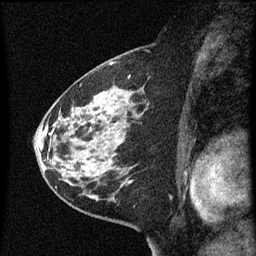
Breast MRI (dynamic contrast-enhanced), one sagittal slice. Position 33 of 60 along the scan axis. Dynamic contrast-enhanced series, image 2 of 3 at this slice position (ordered by acquisition). 1.5 T. TE 4.2 ms, TR 8 ms. 2 mm slice thickness. 256 × 256 image matrix, field of view 180 × 180 mm. Patient: female, 60 years.
Structures marked on this image (semi-automatic segmentation, software-assisted and operator-edited):
- analysis volume of interest (the breast-tissue region the enhancement analysis was run in; not a lesion): bounding box [x1, y1, x2, y2] px = [48, 82, 151, 183]
- tumour enhancement mask (voxels above the 70 % enhancement threshold inside the analysis volume of interest): [51, 110, 133, 183]